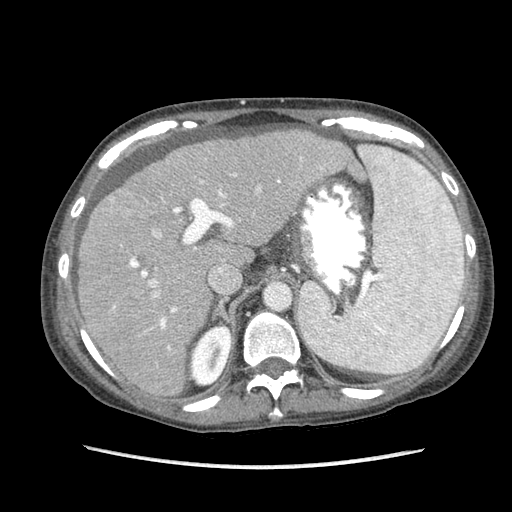
Contrast-enhanced abdominal CT (liver protocol), one axial slice. Position 61 of 87 along the scan axis. 120 kVp. Soft-tissue window (W 400 / L 40 HU). 2.5 mm slice thickness. 512 × 512 image matrix. From the clinical record (not read from this slice): diagnosis: hepatocellular carcinoma (patient treated with transarterial chemoembolisation; whether this scan precedes or follows treatment is not stated here); TNM stage (as recorded): Stage-IIIB; Child-Pugh class: A; tumour differentiation: no biopsy.
Outlined on this slice (semi-automatically segmented with operator editing):
- abdominal aorta: bounding box [x1, y1, x2, y2] px = [265, 284, 290, 309]
- liver parenchyma outside the tumour (the mass and vessels are separate outlines, so this box may not span the whole liver): [78, 130, 352, 396]
- mass: [106, 189, 138, 219]
- liver vessels: [112, 157, 324, 350]